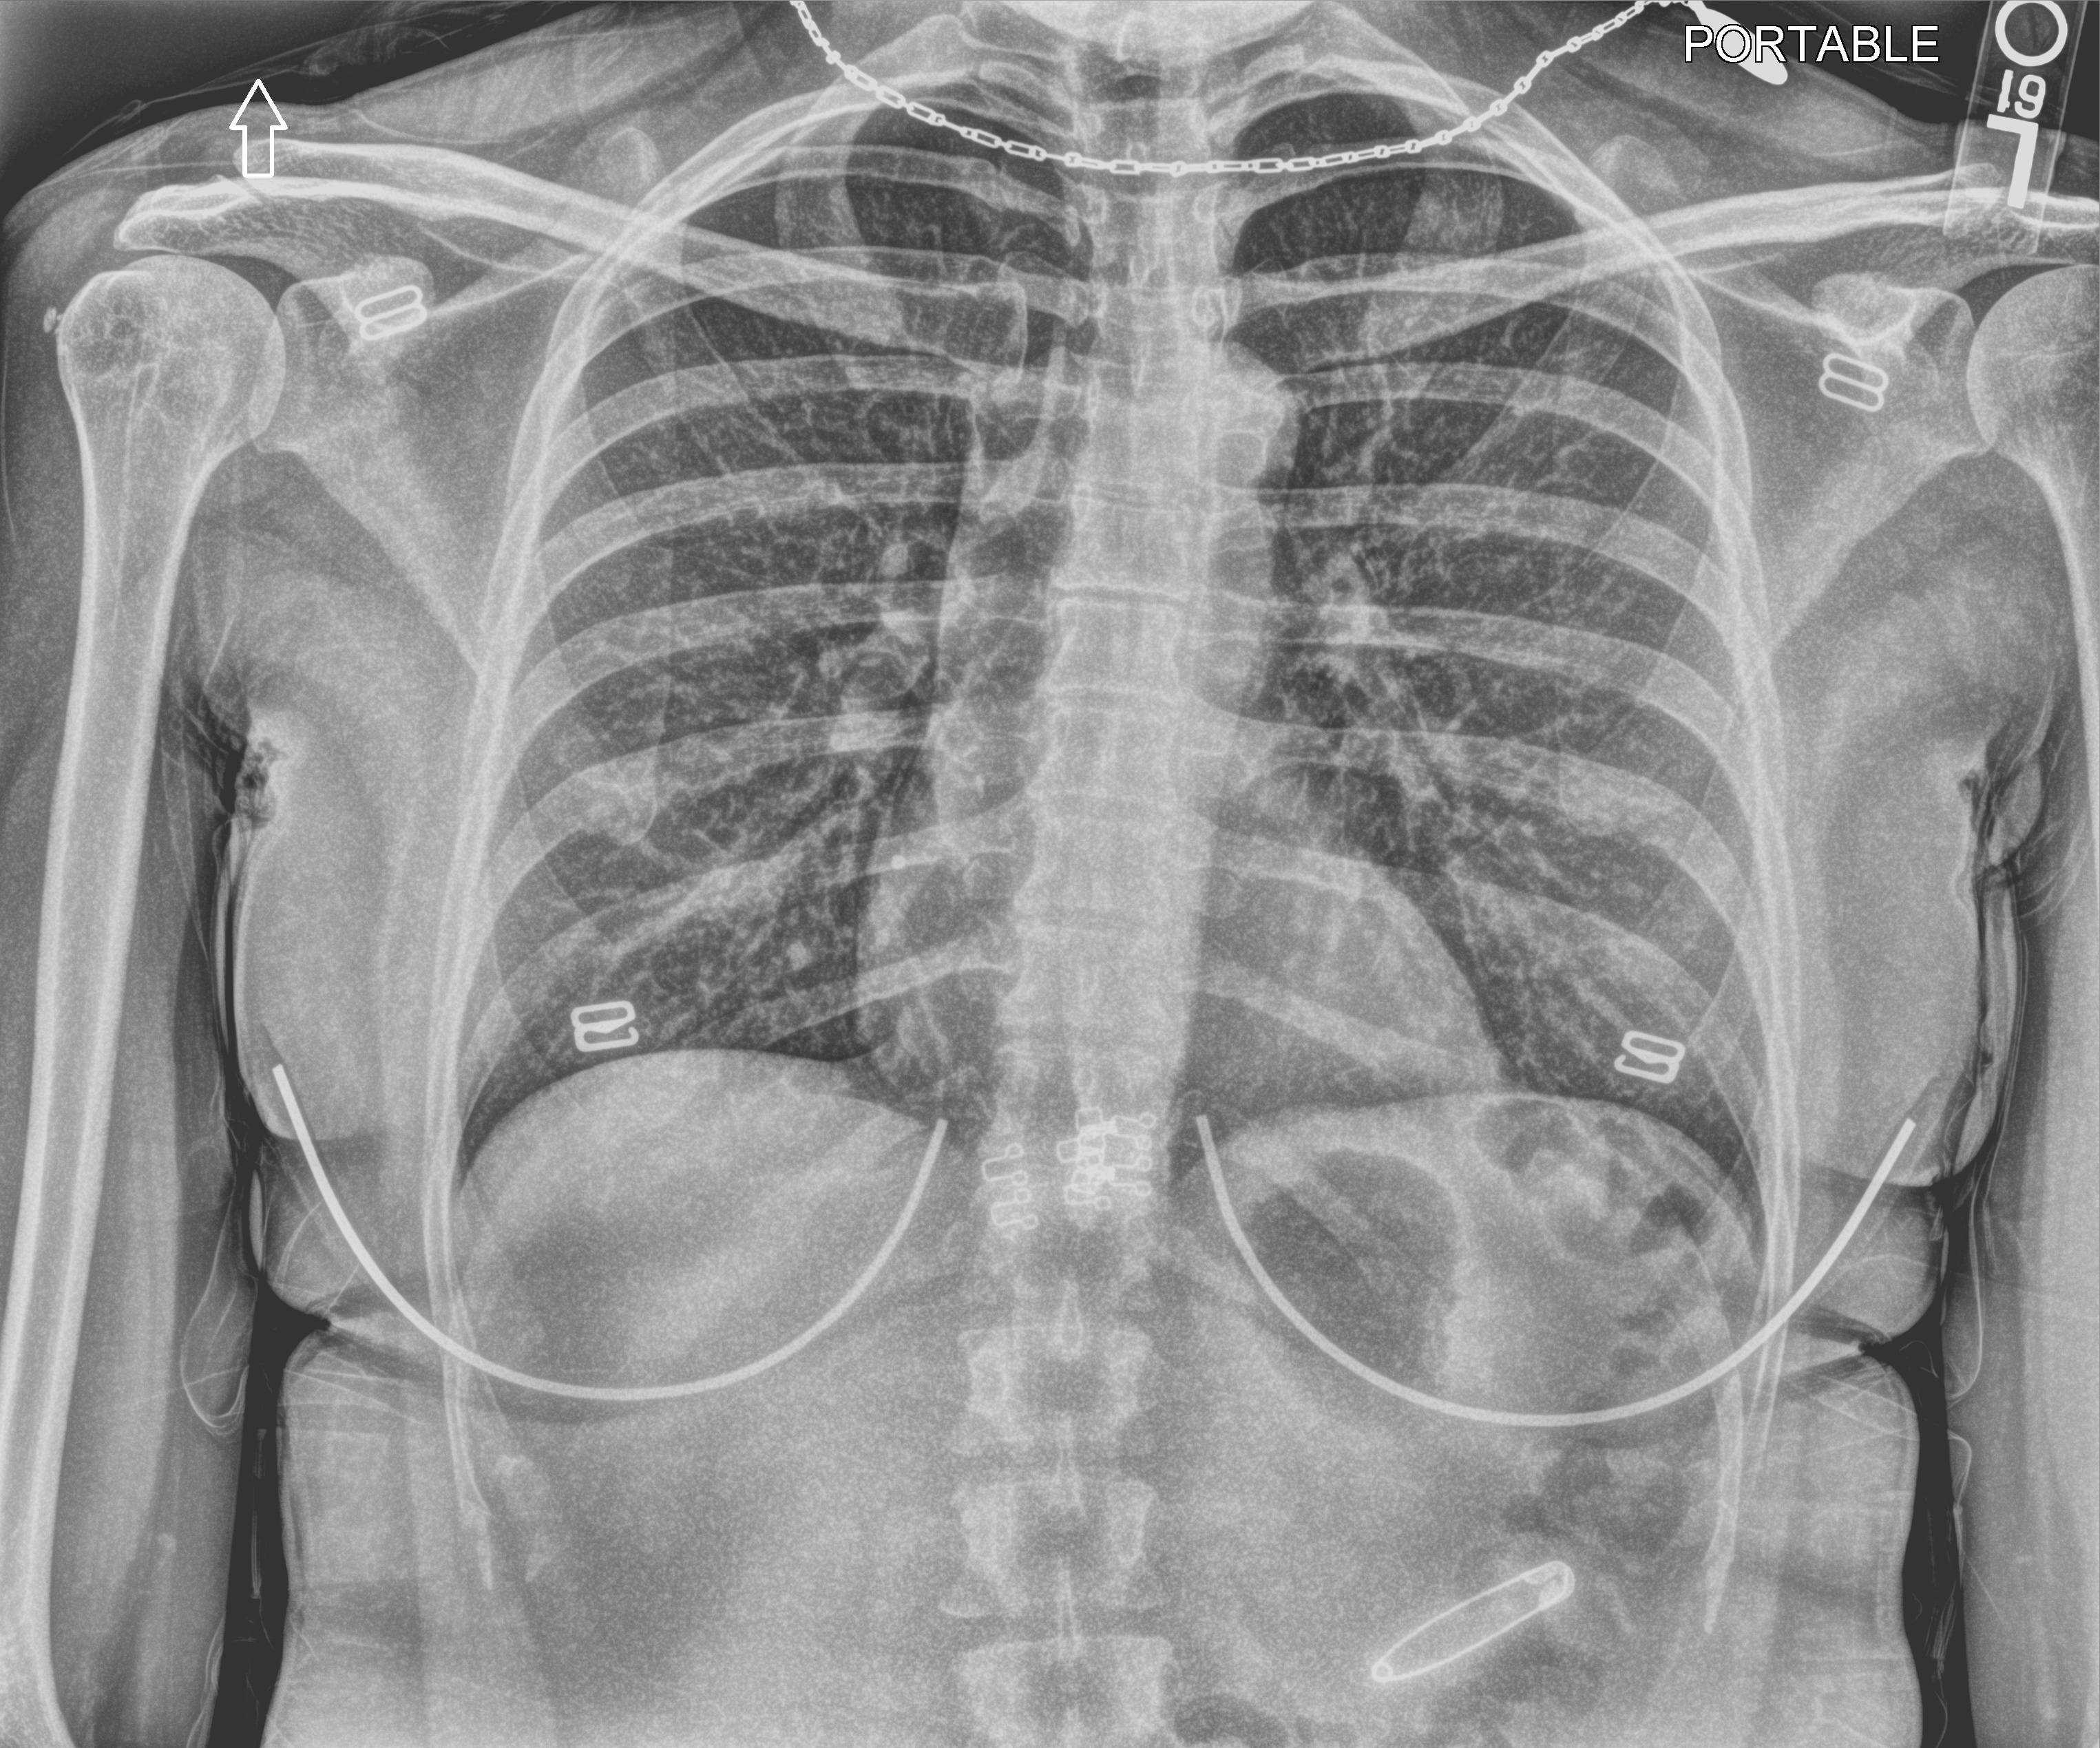
Bedside chest radiograph (computed radiography). Patient hospitalised with COVID-19; female, aged 18–59 years.
Hospital-stay facts (about this admission, not read from this image; timing relative to this image not recorded): admitted to intensive care during this hospital stay: no.